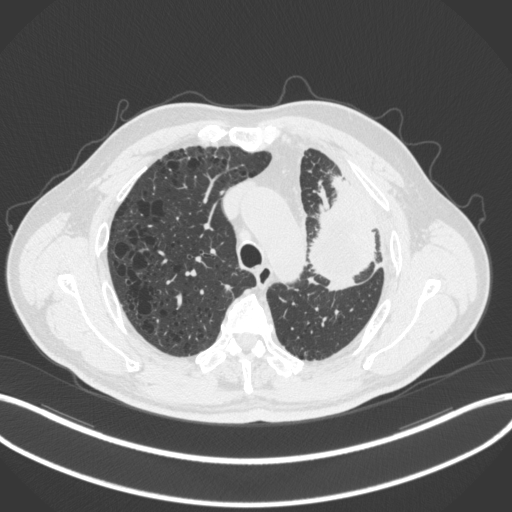
Chest CT, one axial slice; slice 222 of 286 in the series (ordered by position); reconstruction kernel B31f; 120 kVp; lung window (W 1500 / L -600 HU); 1 mm slice thickness; 512 × 512 image matrix, field of view 400 × 400 mm. Patient: male, 68 years. From the clinical record (not read from this slice): clinical TNM (as recorded): T3 N3 M1.
Outlined on this slice (bounding box drawn by a radiologist):
- lung tumour (recorded histology: adenocarcinoma): bounding box [x1, y1, x2, y2] px = [307, 176, 379, 295]